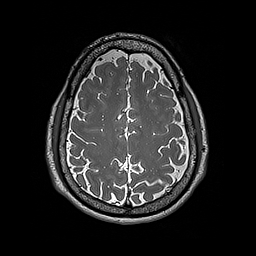
Brain MRI from a brain-tumour surgery series, one axial slice; position 68 of 192 along the scan axis; 1 mm slice thickness; 256 × 256 image matrix, field of view 250 × 250 mm. From the clinical record (not read from this slice): histopathology: Astrocytoma; WHO grade: 2; IDH mutation: yes.
Structures marked on this image (outlined manually by an expert reader):
- tumour: bounding box <160,117,164,119> (left, top, right, bottom; pixels)